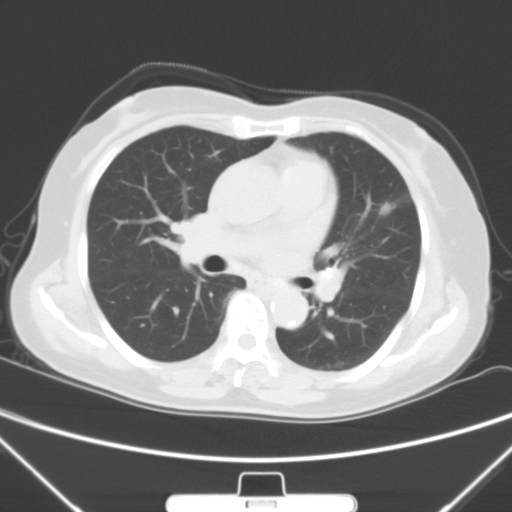
Chest CT, one axial slice; position 31 of 60 along the scan axis; lung window (W 1500 / L -600 HU); 5 mm slice thickness; 512 × 512 image matrix, field of view 350 × 350 mm. Patient: female, 70 years. From the clinical record (not read from this slice): clinical TNM (as recorded): T1b N0 M0; histopathological grade: G2.
Outlined on this slice (bounding box drawn by a radiologist):
- lung tumour (recorded histology: adenocarcinoma): bounding box <376,192,403,230> (left, top, right, bottom; pixels)